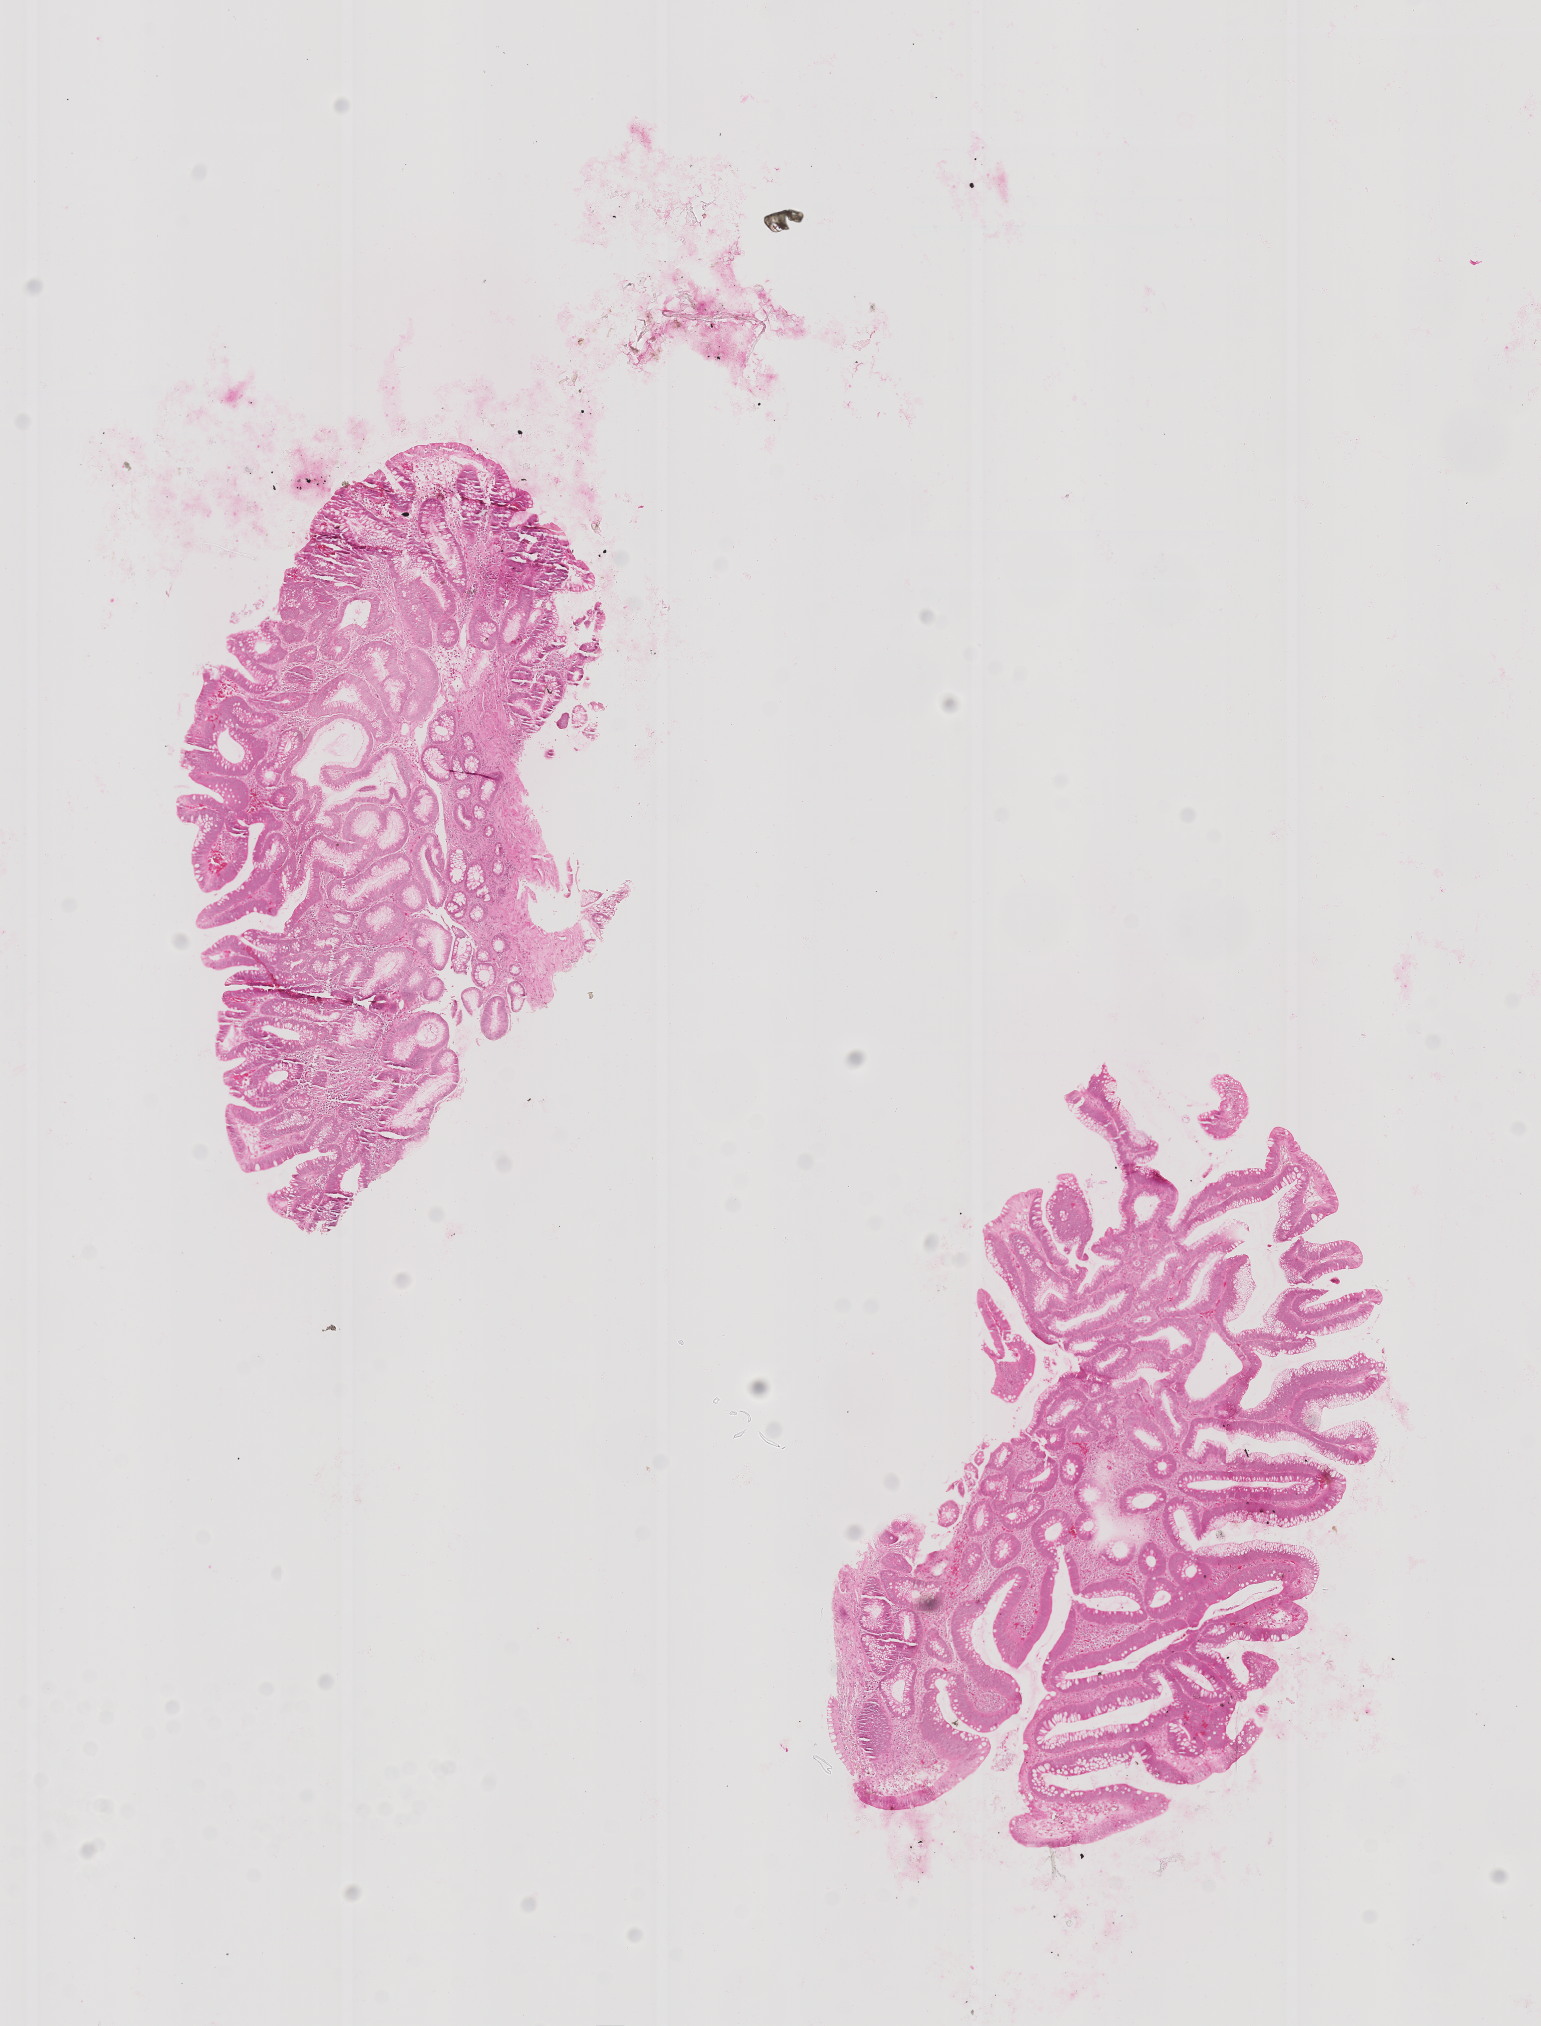
H&E whole-slide image of a colon biopsy, whole scanned area (about 6.2 x 8.1 mm) shown as a low-resolution overview. Formalin-fixed, paraffin-embedded (FFPE) tissue. Site: descending colon. Patient: male.
Lesion category (as recorded): premalignant.